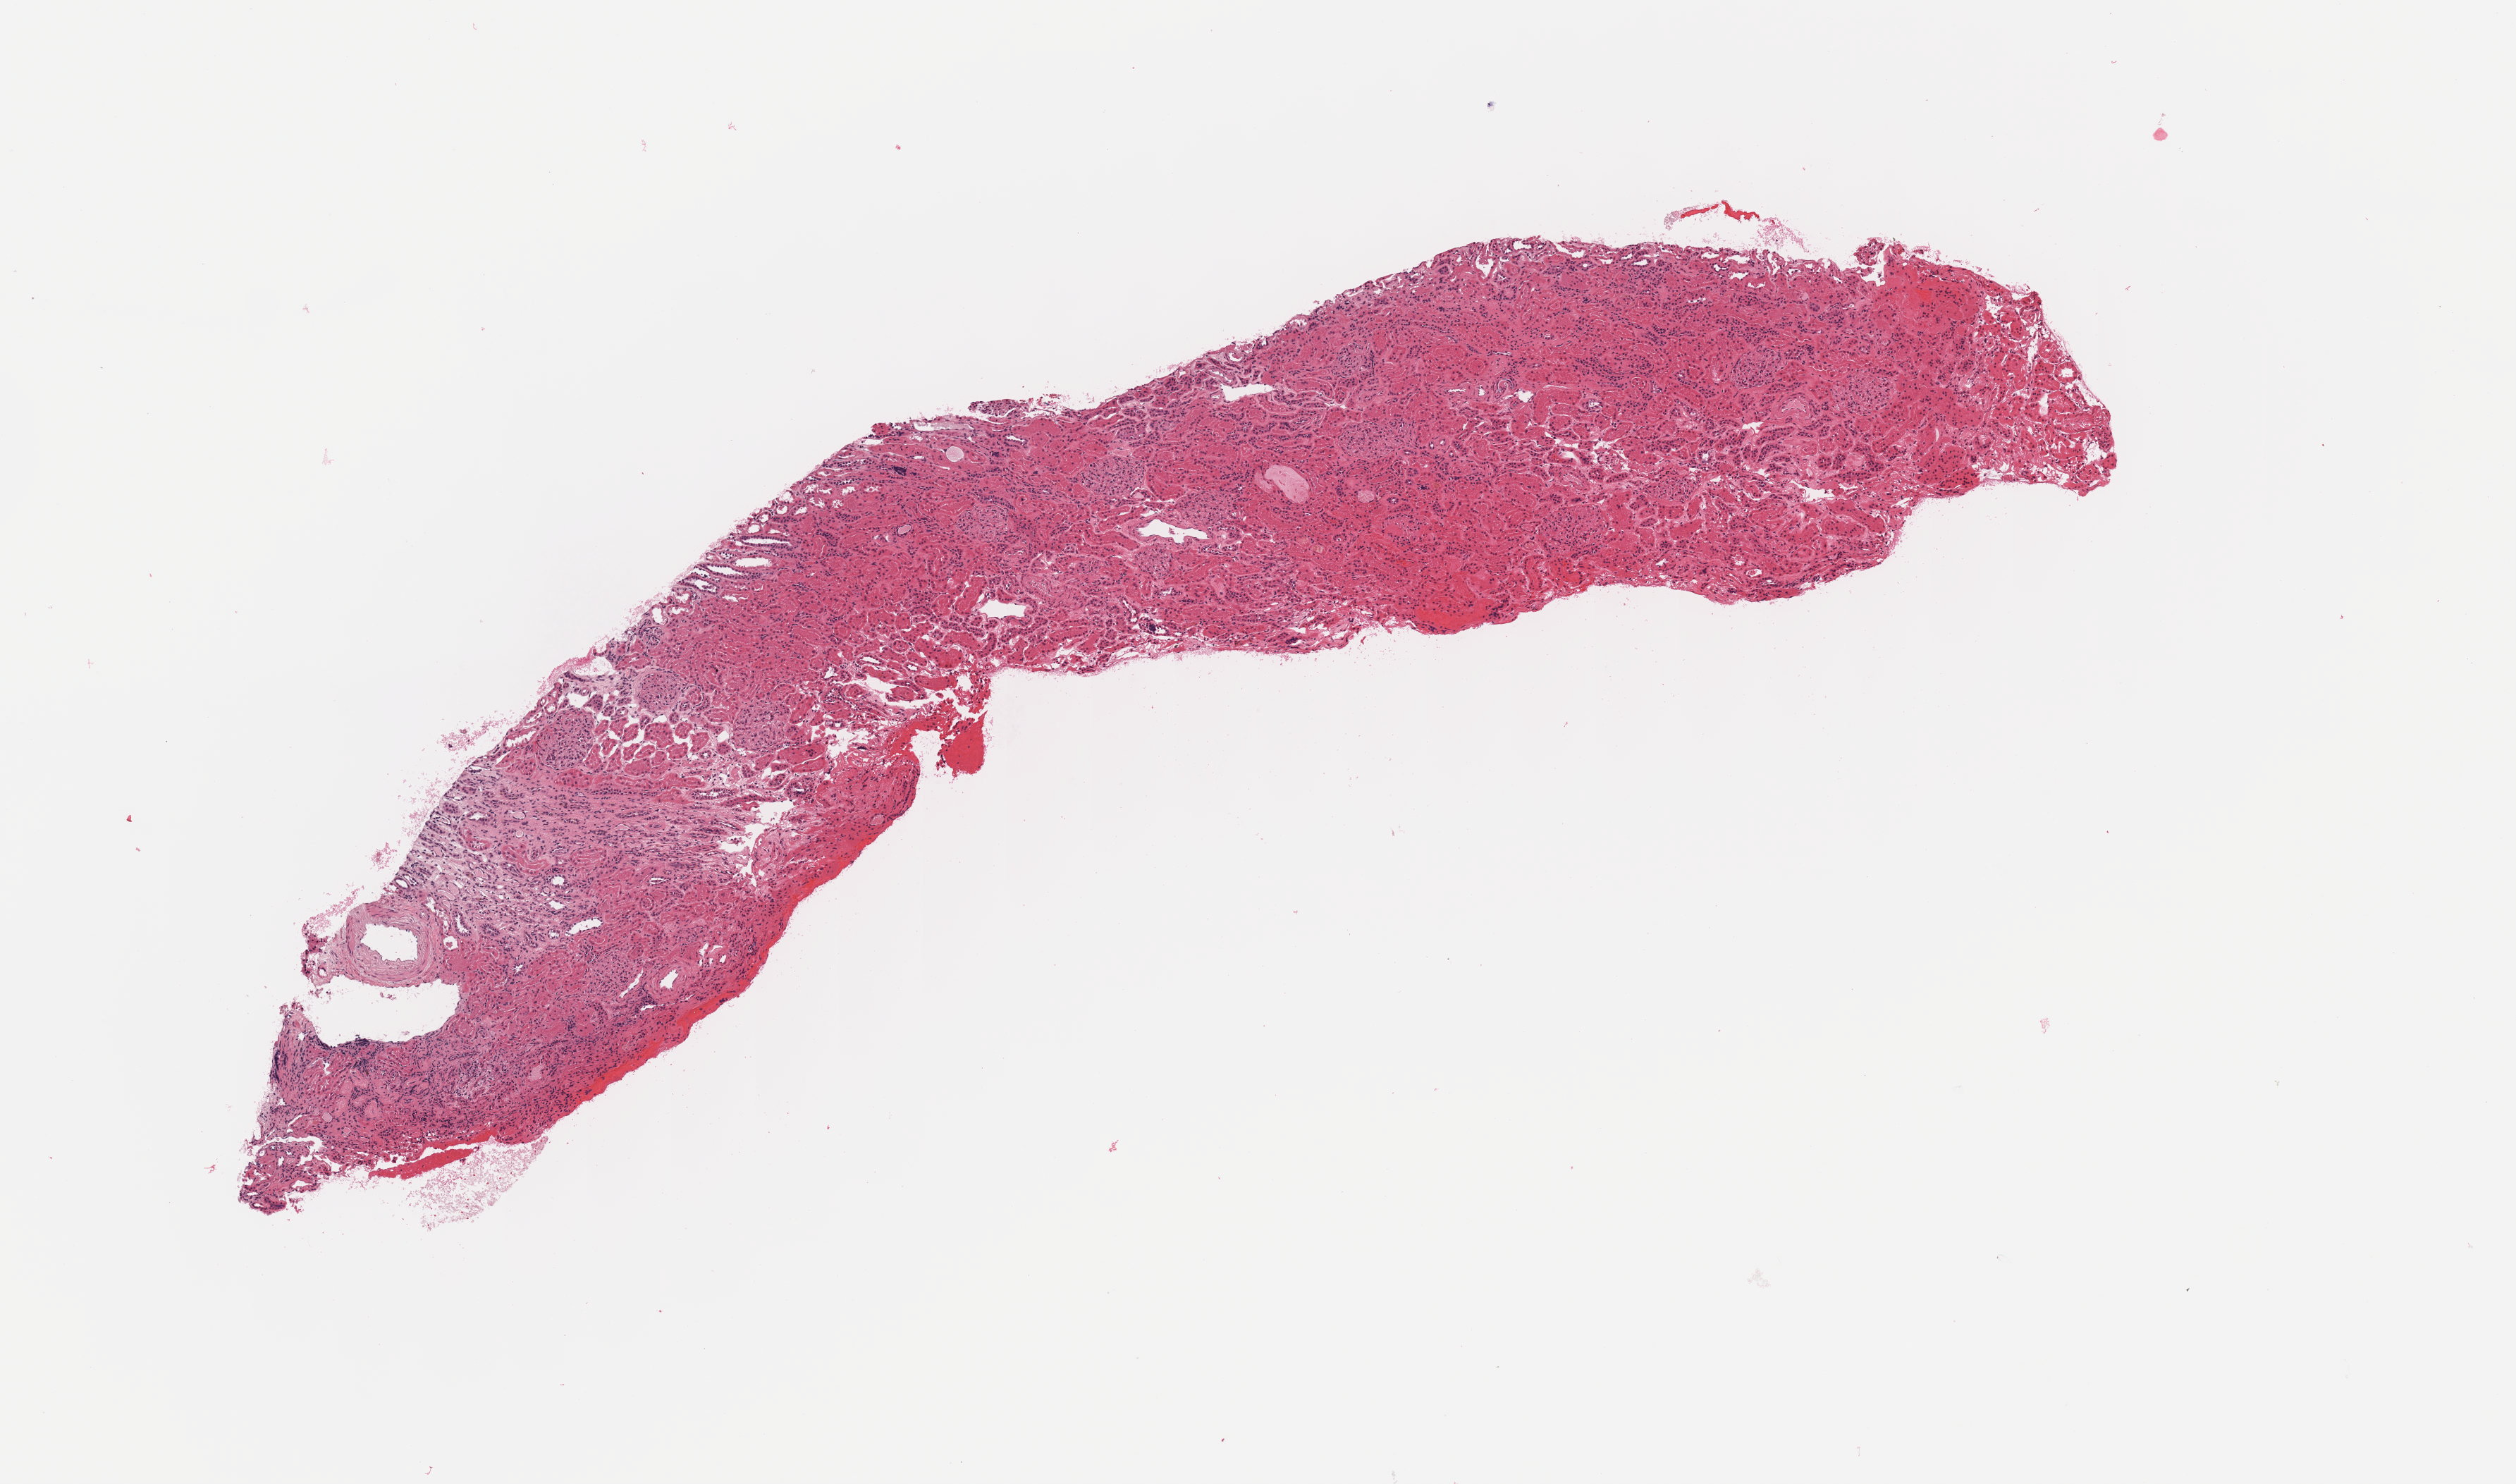
H&E whole-slide image — a low-resolution overview of the entire scanned area, about 7.1 x 4.2 mm, formalin-fixed paraffin-embedded (FFPE) diagnostic section, kidney, solid tissue normal (non-tumour tissue) sample. Male, age 75 years at initial diagnosis. Pathologist review of this section (percent, as recorded): tumour cells 0%, tumour nuclei 0%, normal cells 100%, stromal cells 0%, necrosis 0%. Infiltration values recorded for this section: lymphocyte infiltration 0%, monocyte infiltration 0%, neutrophil infiltration 0%.
- this section: solid tissue normal sample (biorepository sample class)
- patient diagnosis: Renal cell carcinoma, chromophobe type